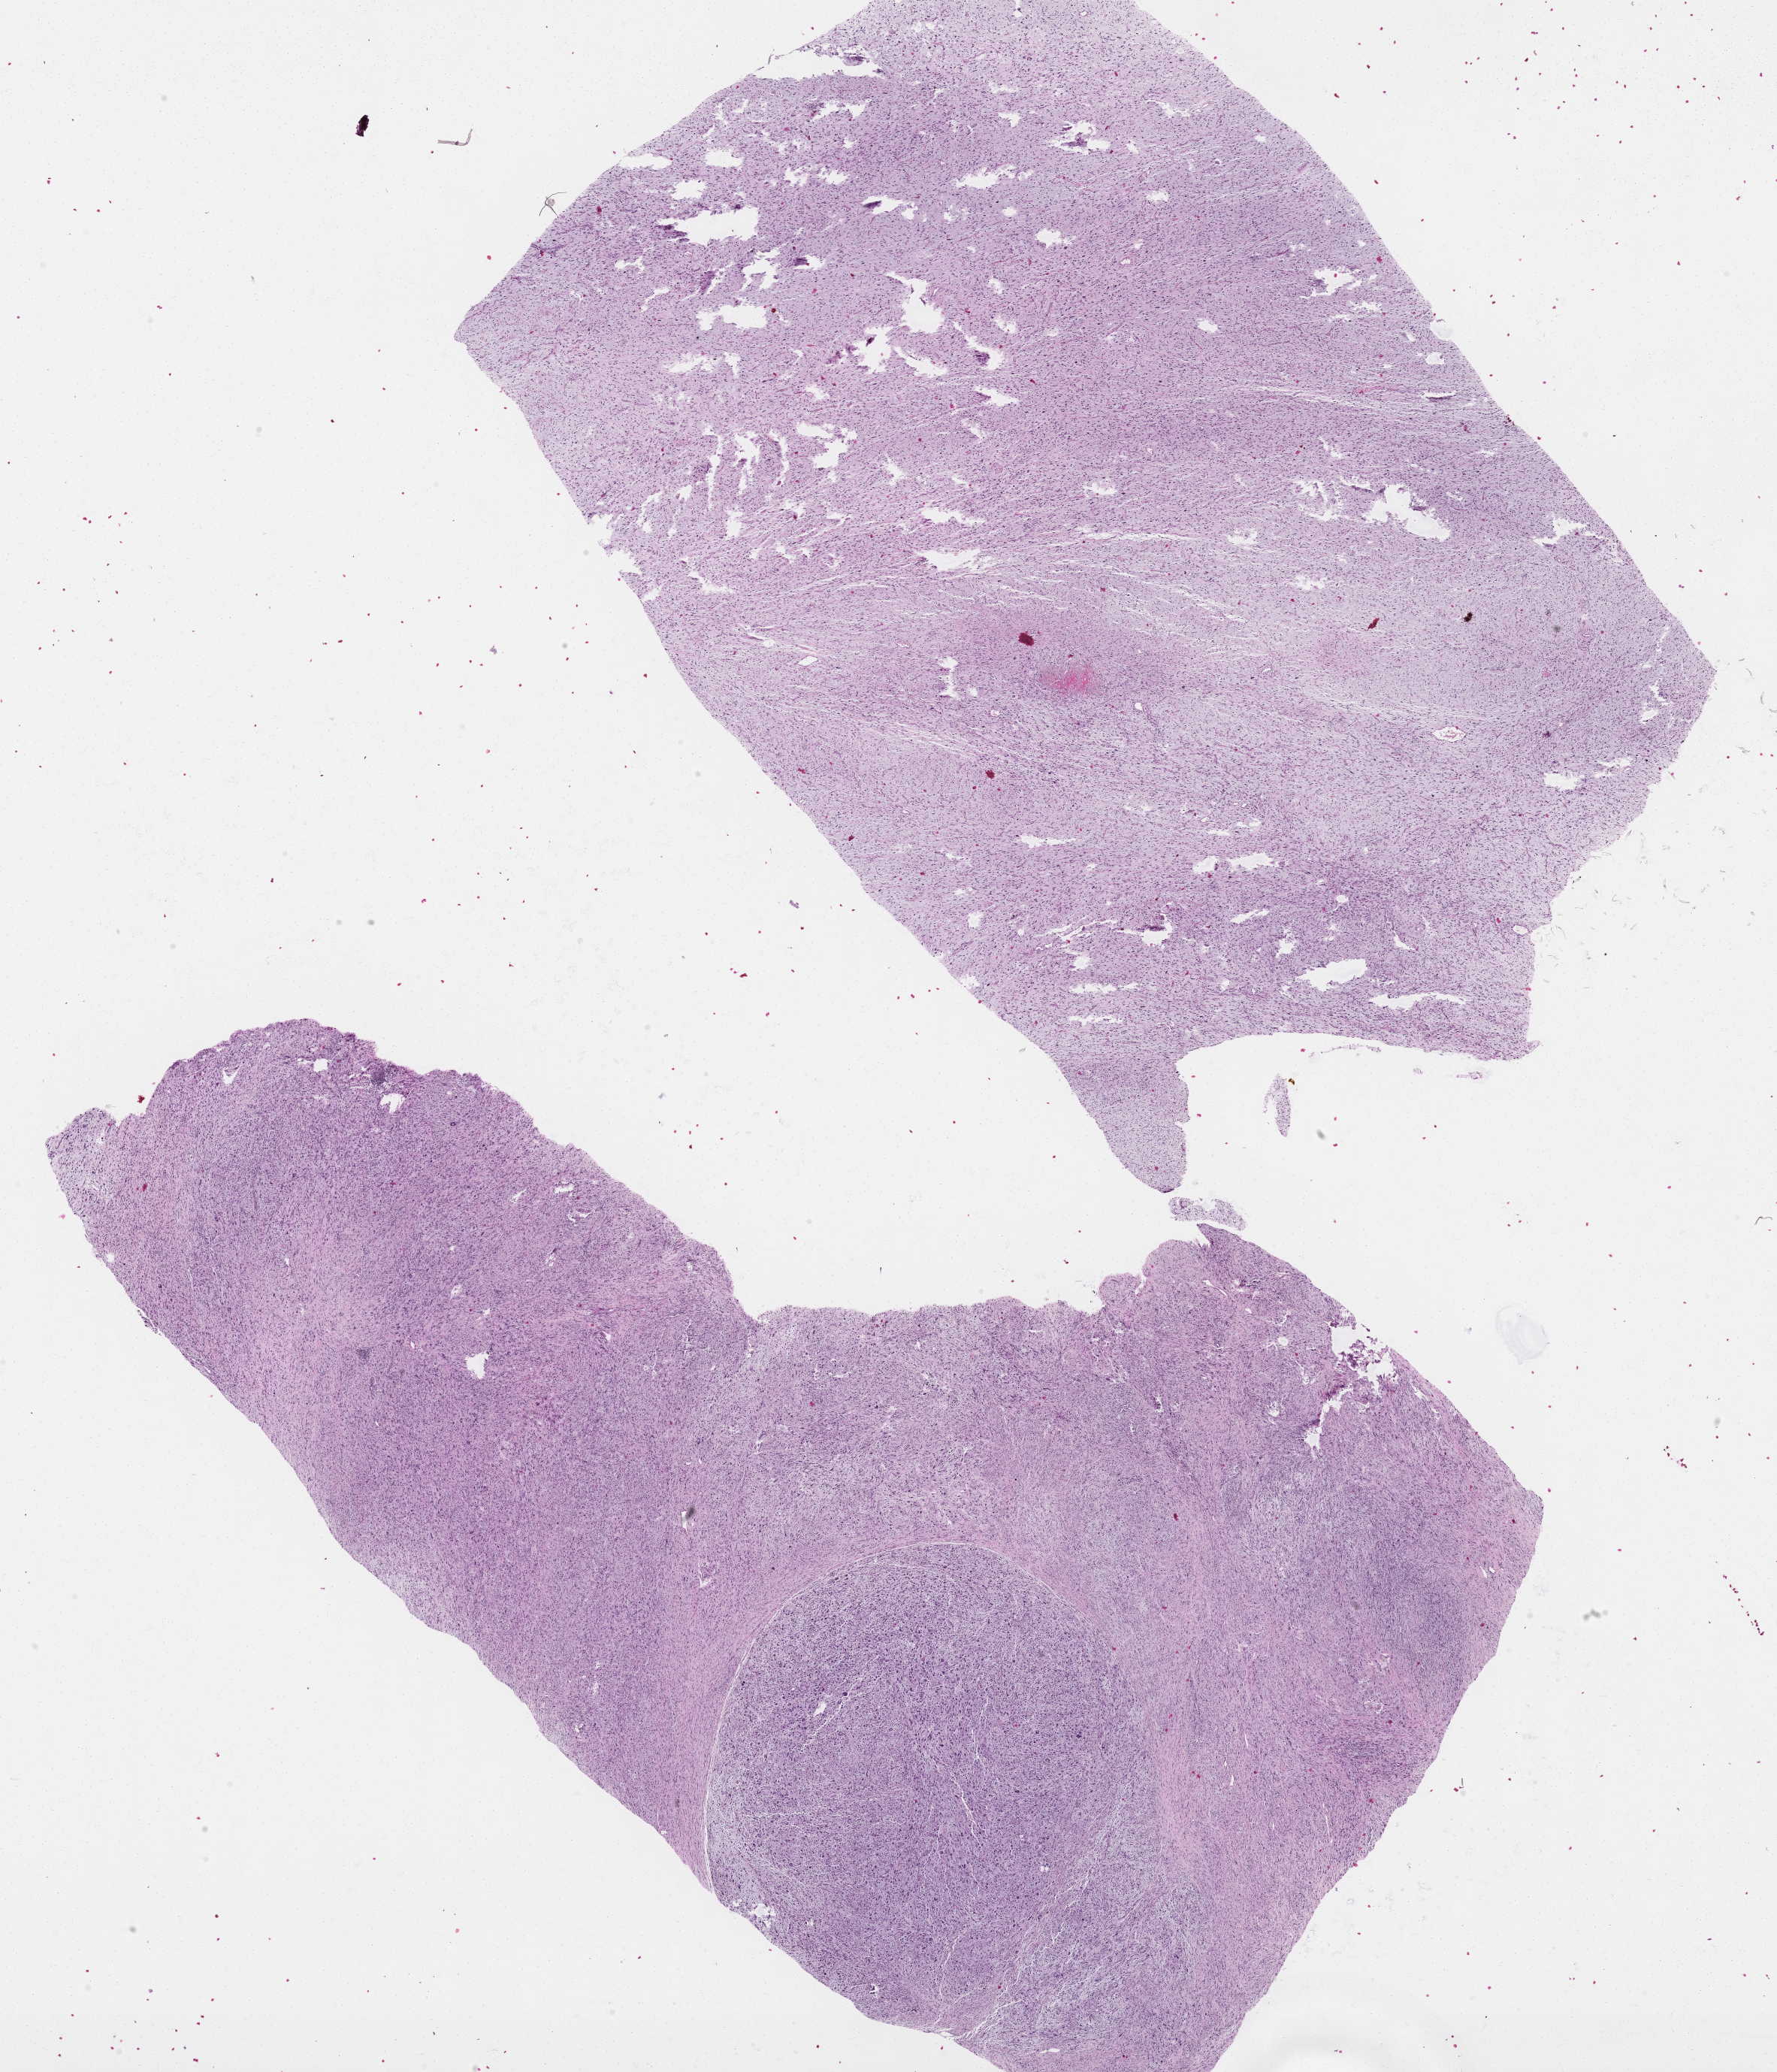
Whole-slide histology image, H&E, whole scanned area (about 19.0 x 22.2 mm, slide scanned at 40x) shown as a low-resolution overview. Formalin-fixed paraffin-embedded (FFPE) diagnostic section. Sample: primary tumour, retroperitoneum and peritoneum. Patient: female, age at initial diagnosis 79 years.
Diagnosis: Fibromyxosarcoma (retroperitoneum).